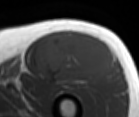
MRI of an extremity soft-tissue mass, one axial slice. MR volume resampled by the dataset authors to the PET/CT grid (not the native acquisition matrix). 3.27 mm slice thickness. 139 × 117 image matrix. Male patient. From the clinical record (not read from this slice): histological type: extraskeletal osteosarcoma; grade: high; site of the primary tumour: thigh.
Outlined on this slice (expert contour drawn on MRI and transferred to this co-registered scan by the dataset authors):
- gross tumour volume (mass): bounding box <36,32,114,83> (left, top, right, bottom; pixels)